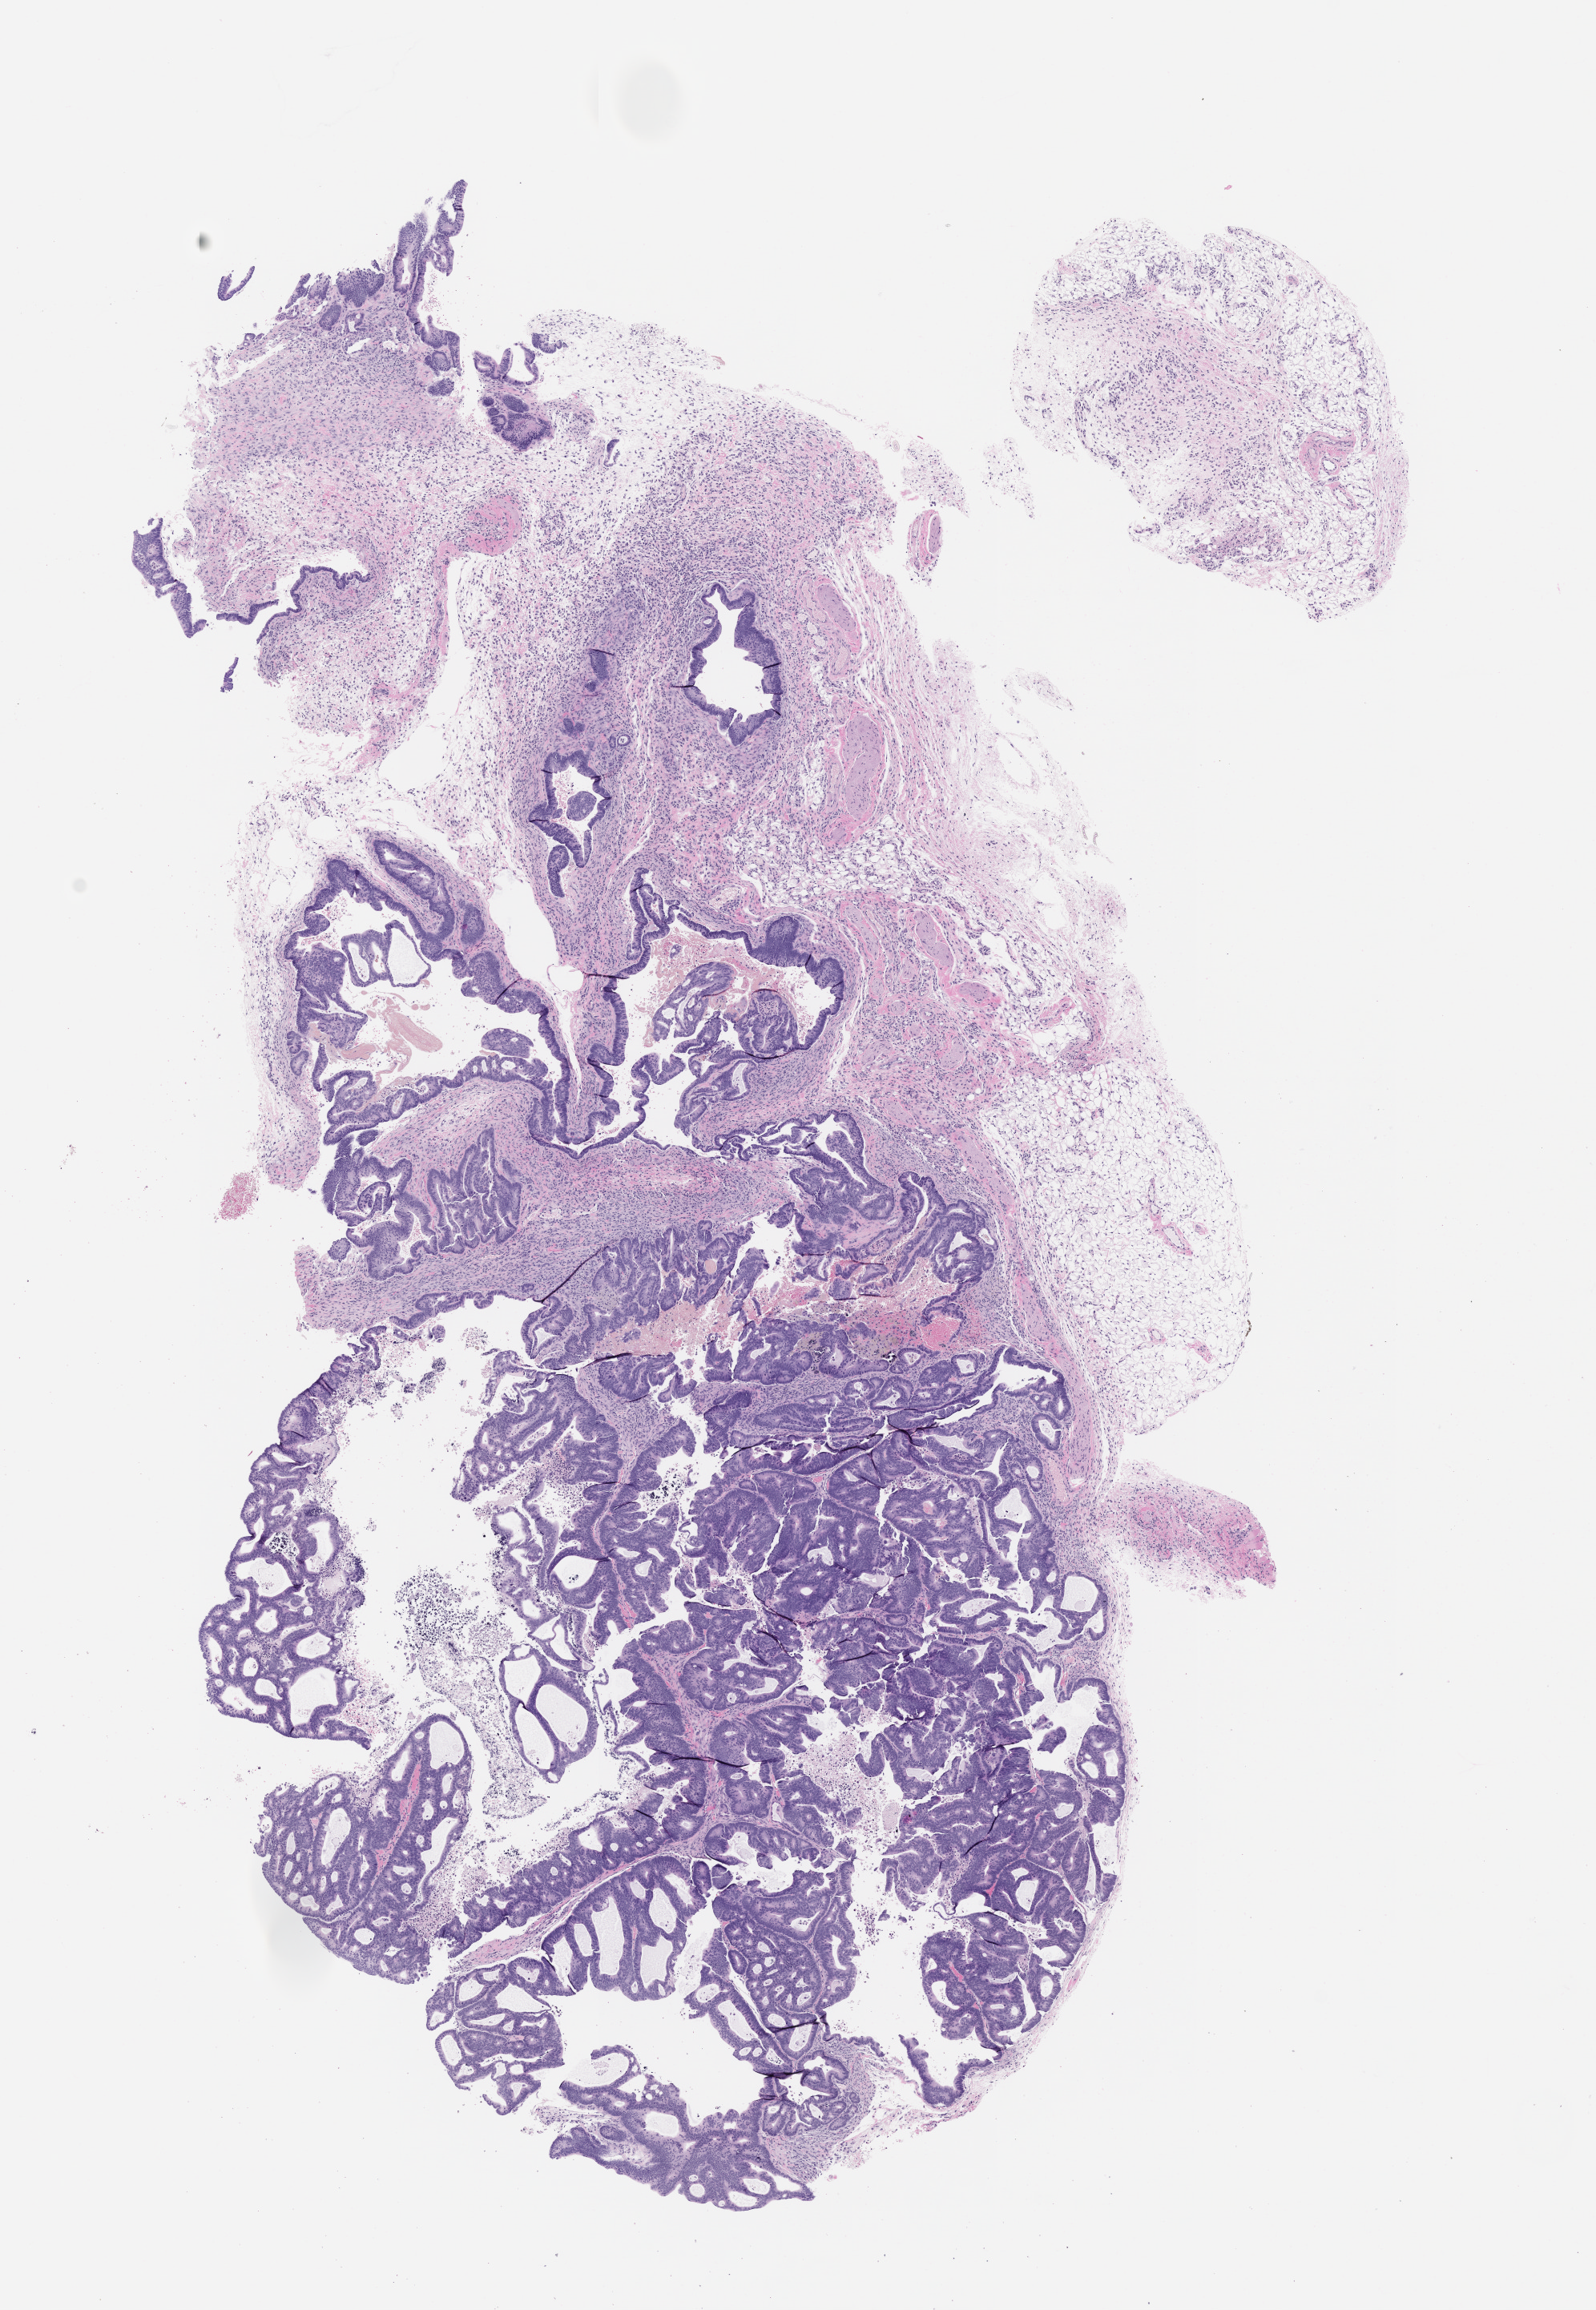
Whole-slide image, hematoxylin and eosin (H&E): patient-derived xenograft (human tumor grown in a mouse), passage 1, shown as a low-resolution overview of the whole scanned area (about 8.0 x 11.6 mm); formalin-fixed, paraffin-embedded (FFPE) tissue; tumor site category: colon.
Originating patient diagnosis: Colon Adenocarcinoma.